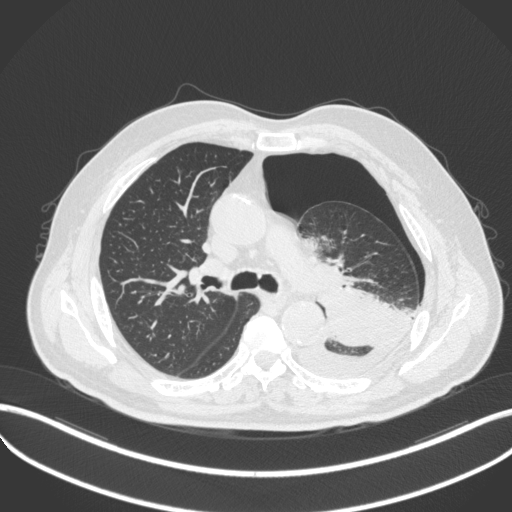
Chest CT, one axial slice. Position 332 of 466 along the scan axis. Reconstruction kernel B31f. 120 kVp. Lung window (W 1500 / L -600 HU). 1 mm slice thickness. 512 × 512 image matrix, field of view 400 × 400 mm. Patient: male, 76 years. From the clinical record (not read from this slice): clinical TNM (as recorded): T3 N0 M1b.
Structures marked on this image (rectangle marked by the reading radiologist):
- lung tumour (recorded histology: adenocarcinoma): bounding box (x1, y1, x2, y2) in pixels: (312, 279, 400, 347)